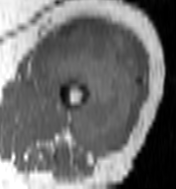
MRI of an extremity soft-tissue mass, one axial slice. MR volume resampled by the dataset authors to the PET/CT grid (not the native acquisition matrix). 3.27 mm slice thickness. 176 × 189 image matrix, field of view 172 × 185 mm. Female patient. Case-level facts recorded for this patient, not image findings: histological type: undifferentiated – high grade; grade: high; site of the primary tumour: left thigh.
Annotated regions visible in this slice (expert contour drawn on MRI and transferred to this co-registered scan by the dataset authors):
- gross tumour volume including surrounding oedema: box from (x=44, y=25) to (x=141, y=158) px
- gross tumour volume (mass): (x=44, y=25)–(x=141, y=158)